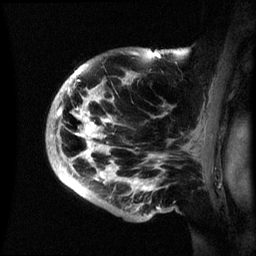
Breast MRI (dynamic contrast-enhanced), one sagittal slice. Position 45 of 60 along the scan axis. Dynamic contrast-enhanced series, image 2 of 3 at this slice position (ordered by acquisition). 1.5 T. TE 4.2 ms, TR 8.4 ms. 2.4 mm slice thickness. 256 × 256 image matrix, field of view 230 × 230 mm. Patient: female, 48 years.
Outlined on this slice (semi-automatically segmented with operator editing):
- analysis volume of interest (the breast-tissue region the enhancement analysis was run in; not a lesion): bounding box (x1, y1, x2, y2) in pixels: (47, 49, 193, 221)
- tumour enhancement mask (voxels above the 70 % enhancement threshold inside the analysis volume of interest): (61, 52, 157, 189)